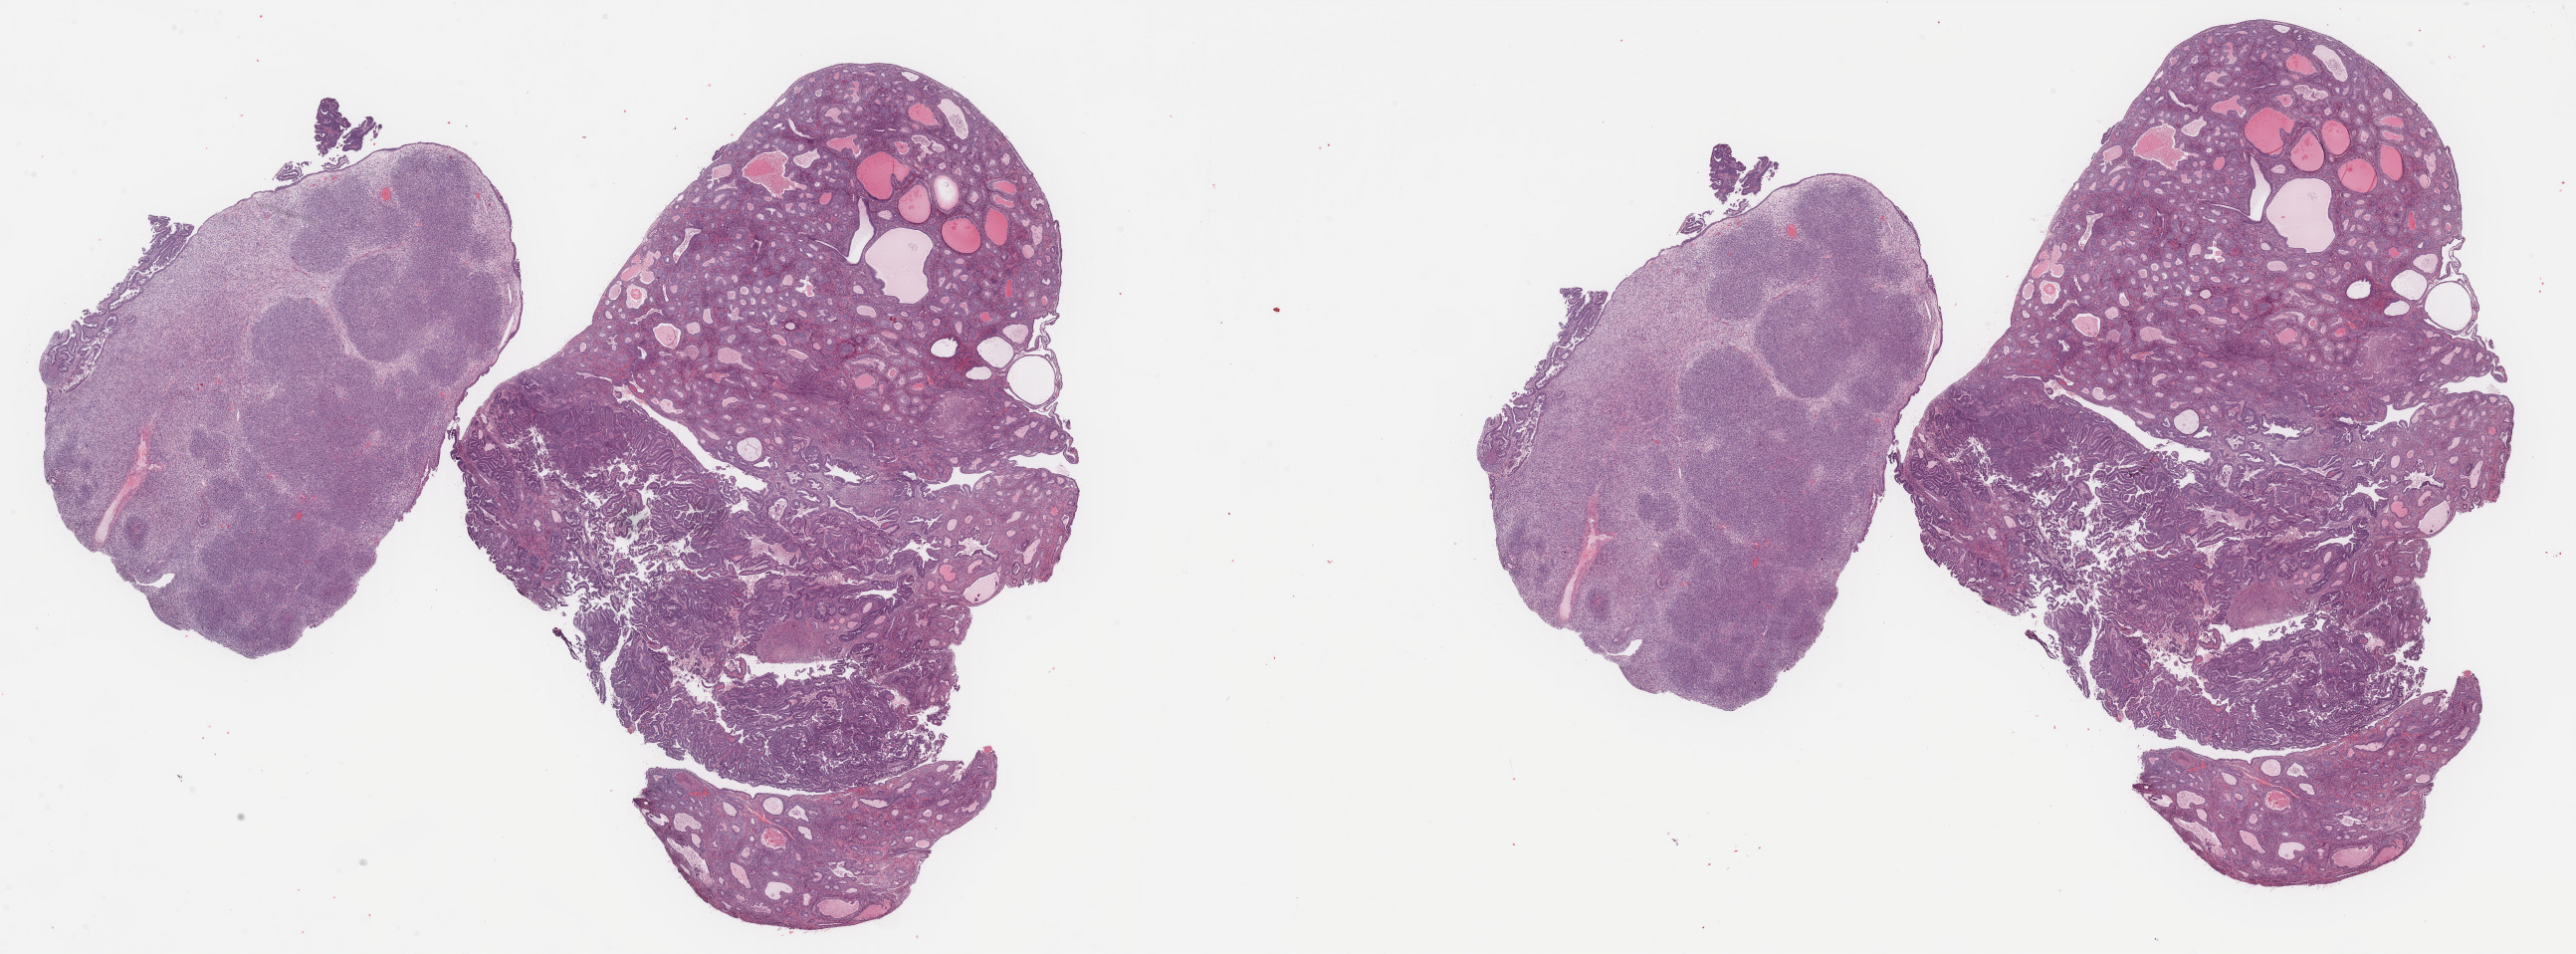
Hematoxylin and eosin (H&E) stained whole-slide image — whole scanned area (about 40.9 x 15.2 mm, slide scanned at 40x) shown as a low-resolution overview; FFPE section; uterus, primary tumour sample. Patient: female, age at initial diagnosis 73 years.
Histologic diagnosis: Carcinosarcoma, NOS (fundus uteri). FIGO stage: IB.